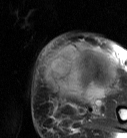
MRI of an extremity soft-tissue mass, one axial slice. Position 21 of 87 along the scan axis. T2-weighted fat-saturated. MR volume resampled by the dataset authors to the PET/CT grid (not the native acquisition matrix). 3.27 mm slice thickness. 127 × 138 image matrix, field of view 124 × 135 mm. Female patient. From the clinical record (not read from this slice): histological type: pleiomorphic leiomyosarcoma; grade: high; site of the primary tumour: left biceps.
Outlined on this slice (expert contour drawn on MRI and transferred to this co-registered scan by the dataset authors):
- gross tumour volume including surrounding oedema: bounding box (x1, y1, x2, y2) in pixels: (43, 43, 117, 104)
- gross tumour volume (mass): (43, 43, 117, 101)